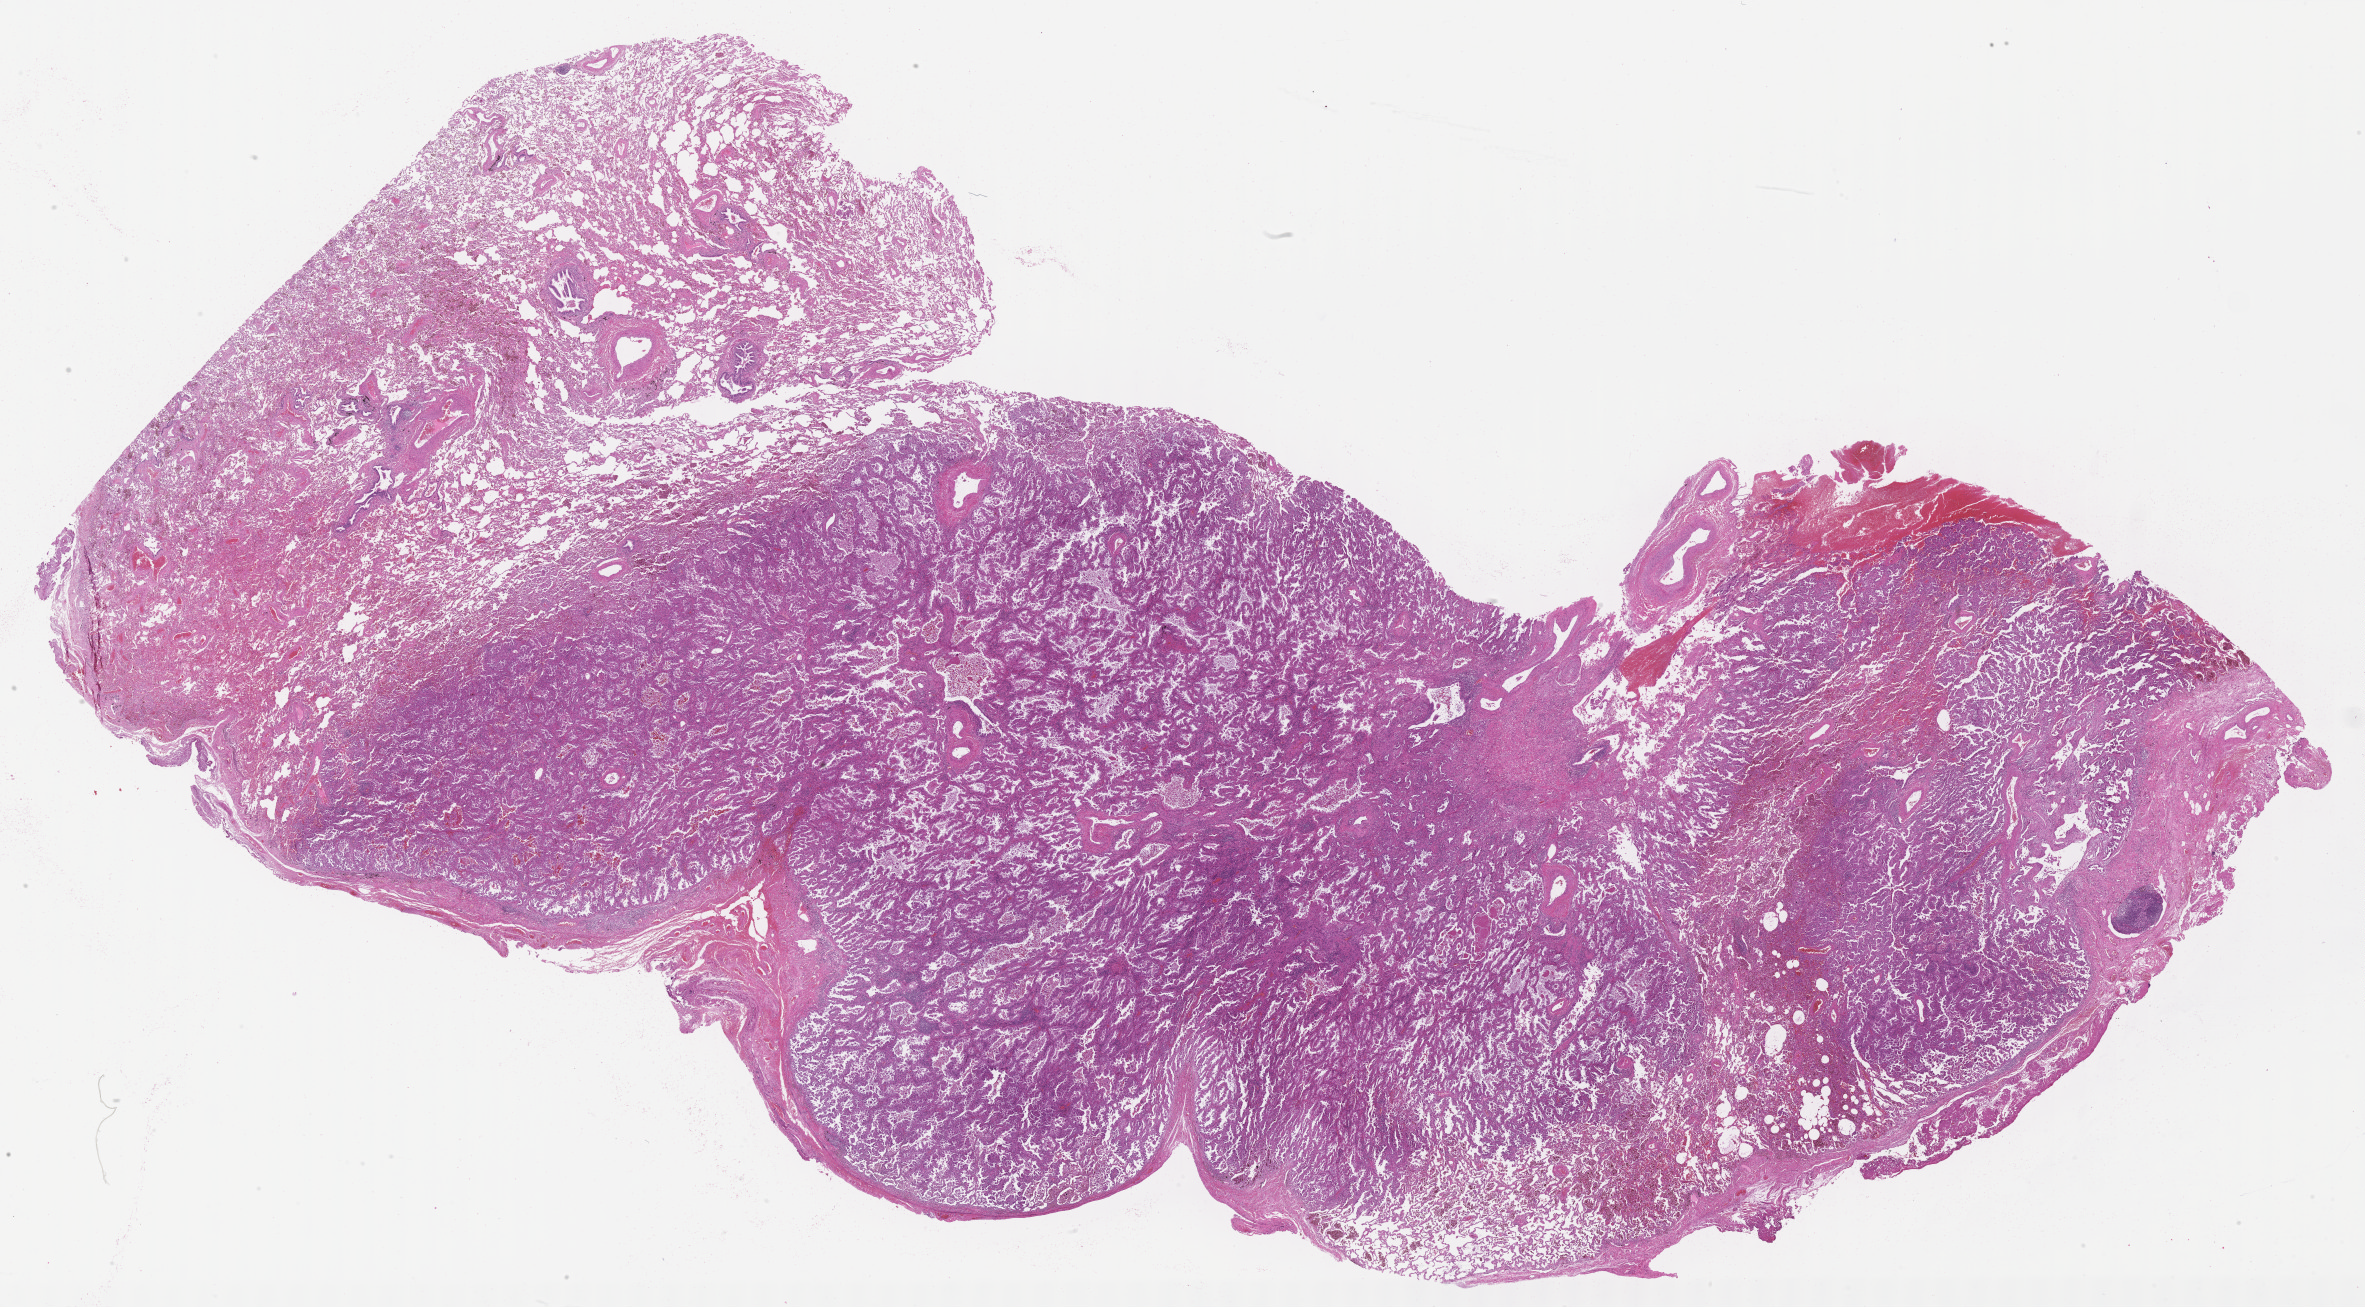
Whole-slide image, H&E stain, low-resolution overview of the scanned area, about 38.2 x 21.1 mm, formalin-fixed paraffin-embedded section, specimen: primary tumor, anatomic site: lower lobe of right lung. Male patient, 56 years old. Slide review estimates, as recorded: tumor cells 75%, tumor nuclei 75%, stromal cells 24%, necrosis 1%, normal cells 0%. Inflammatory infiltration, as recorded: lymphocyte infiltration 4%, monocyte infiltration 4%, neutrophil infiltration 6%.
* histologic diagnosis: Adenocarcinoma, NOS
* section: top of the tissue portion
* AJCC pathologic stage: Stage IA